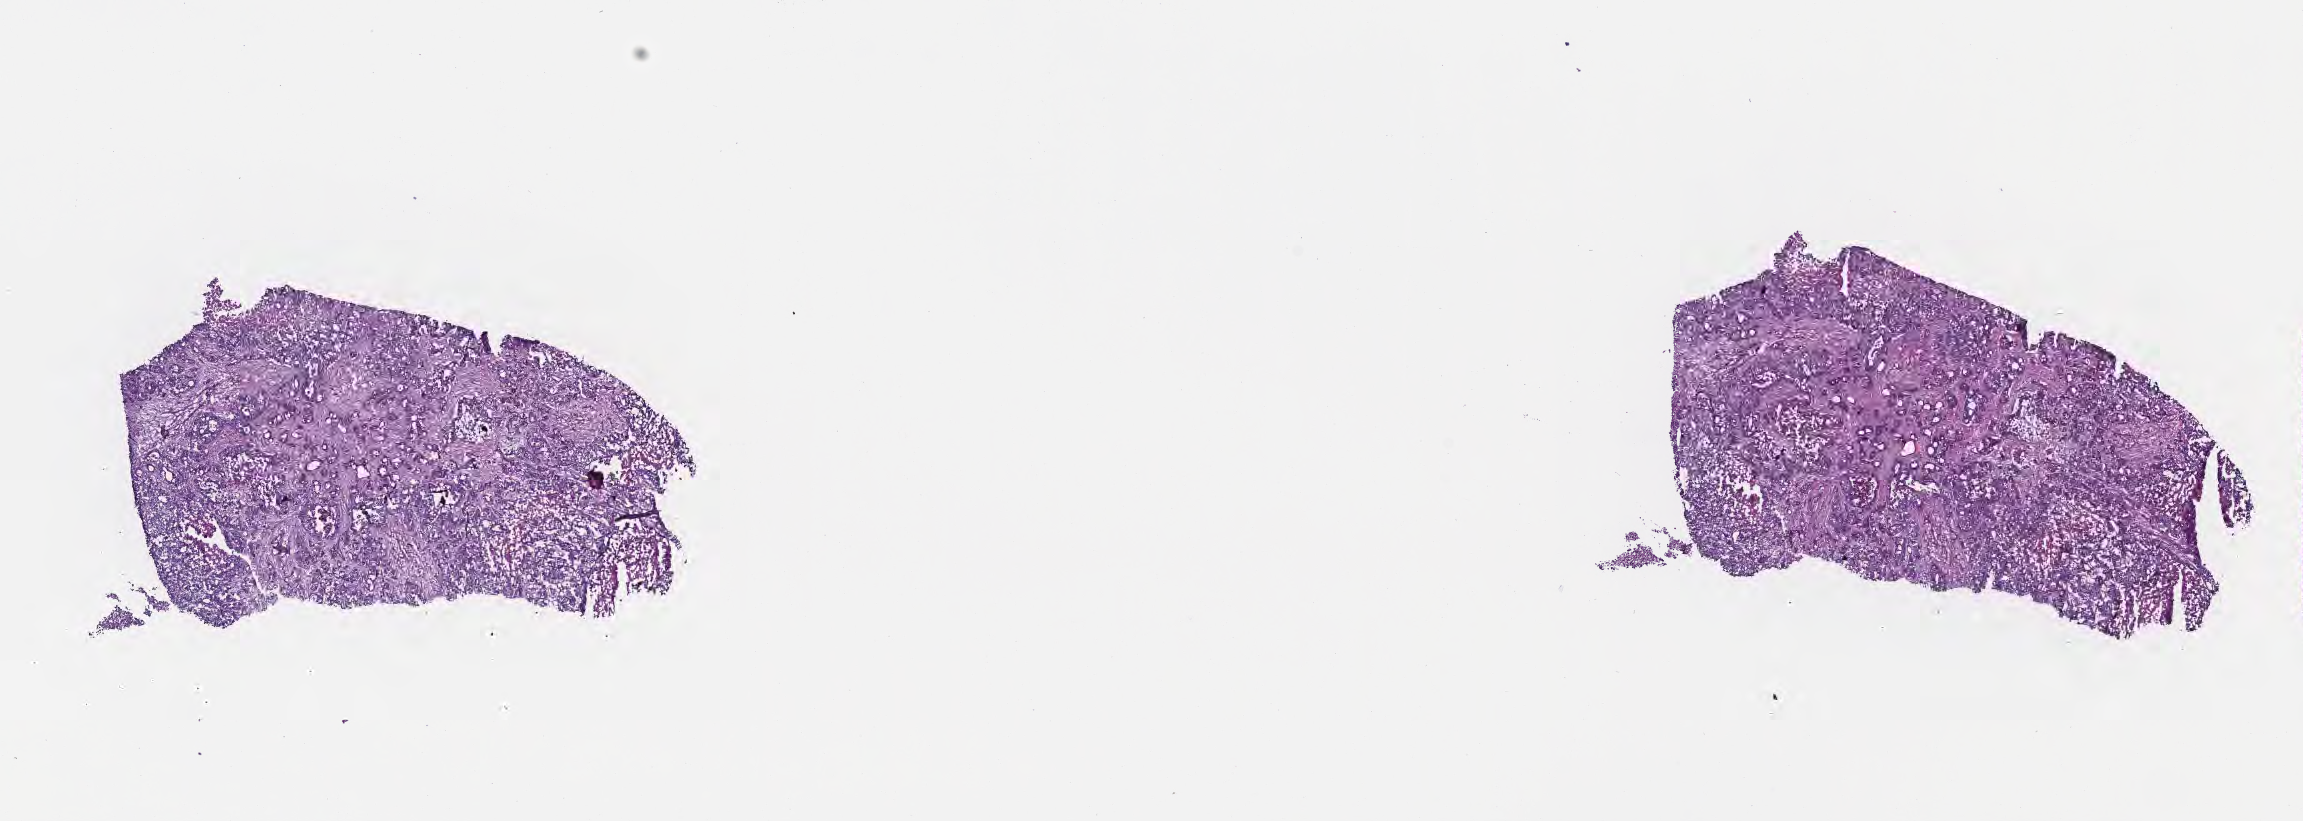
Whole-slide image, H&E stain, a low-resolution overview of the entire scanned area, about 18.6 x 6.6 mm. Frozen section (tissue freezing medium). Metastatic tumor tissue, resected from liver. Patient: male, age at initial diagnosis 69 years. Composition of this section per pathologist review: tumor cells 70%, tumor nuclei 80%, stromal cells 30%, necrosis 0%, normal cells 0%. Infiltration values recorded for this section: lymphocyte infiltration 0%, monocyte infiltration 0%, neutrophil infiltration 0%.
- section: bottom of the tissue portion
- patient diagnosis (primary): Adenocarcinoma, NOS